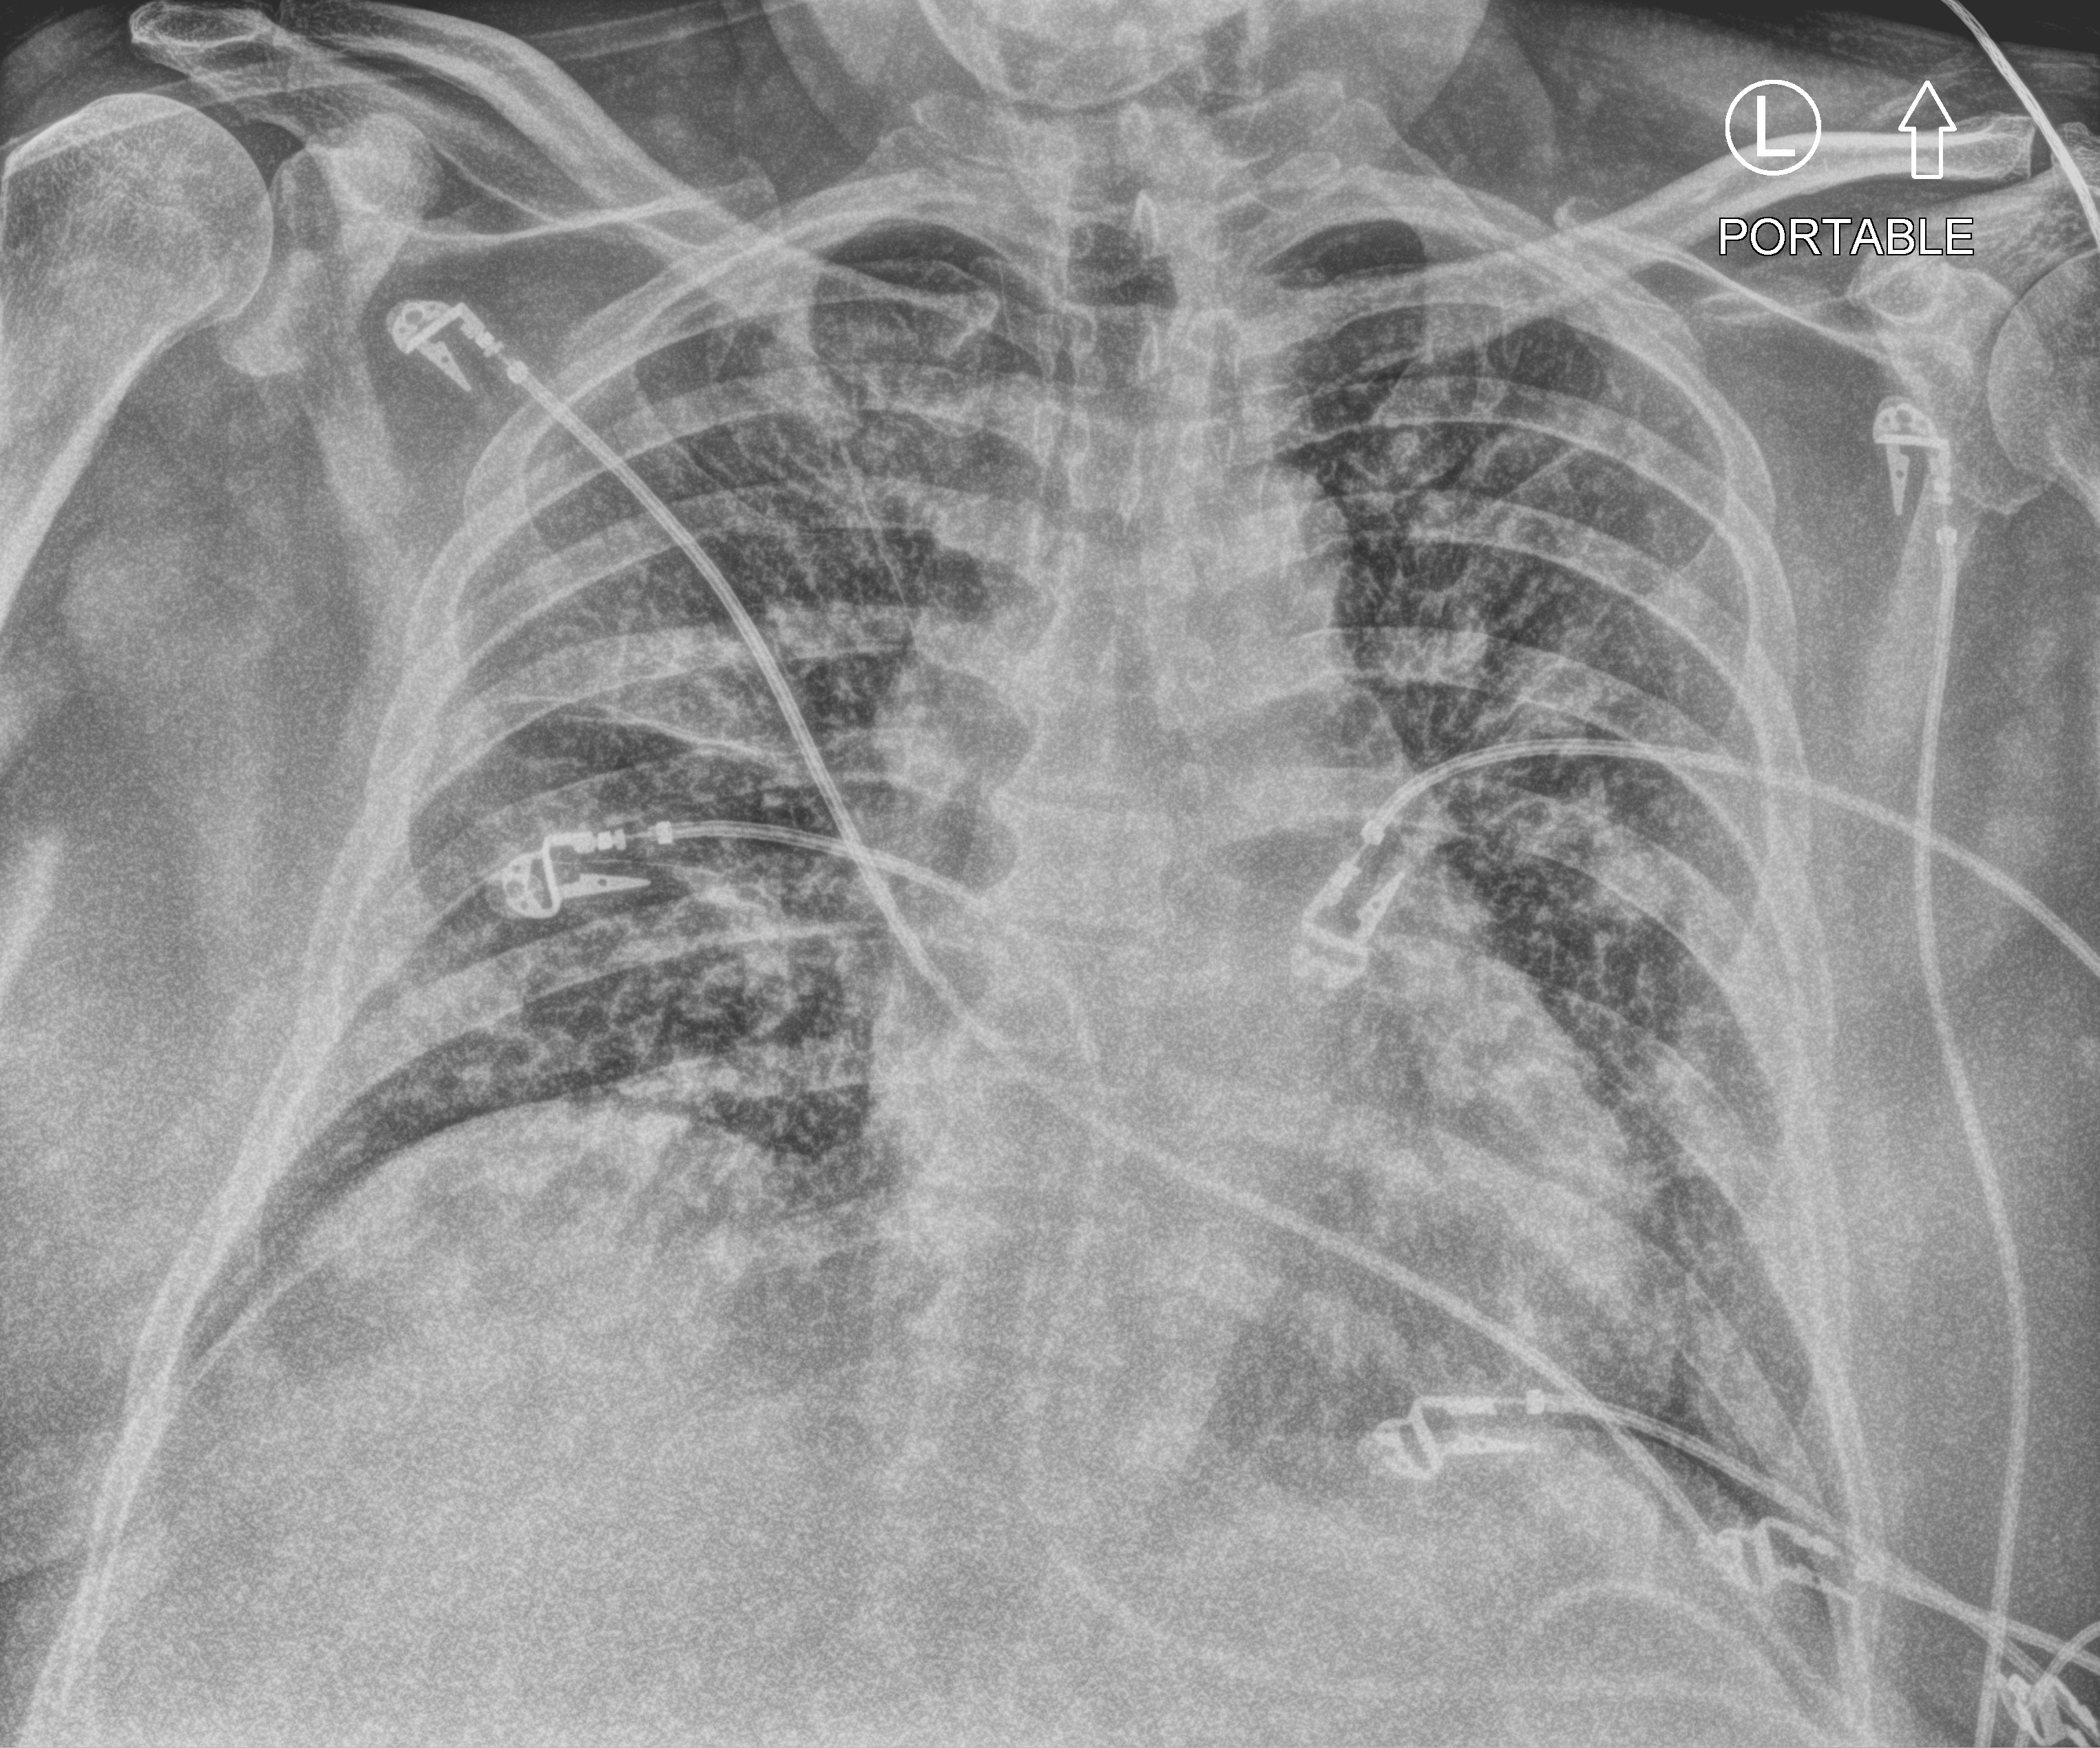
Portable chest radiograph, anteroposterior (AP) projection. Male patient hospitalised with COVID-19, age 60–74 years.
From the hospital-stay record, not from the radiograph (when in the stay this image was taken is not recorded):
- admitted to intensive care during this hospital stay: yes
- mechanically ventilated during this hospital stay: yes
- chronic kidney disease (admission record): no